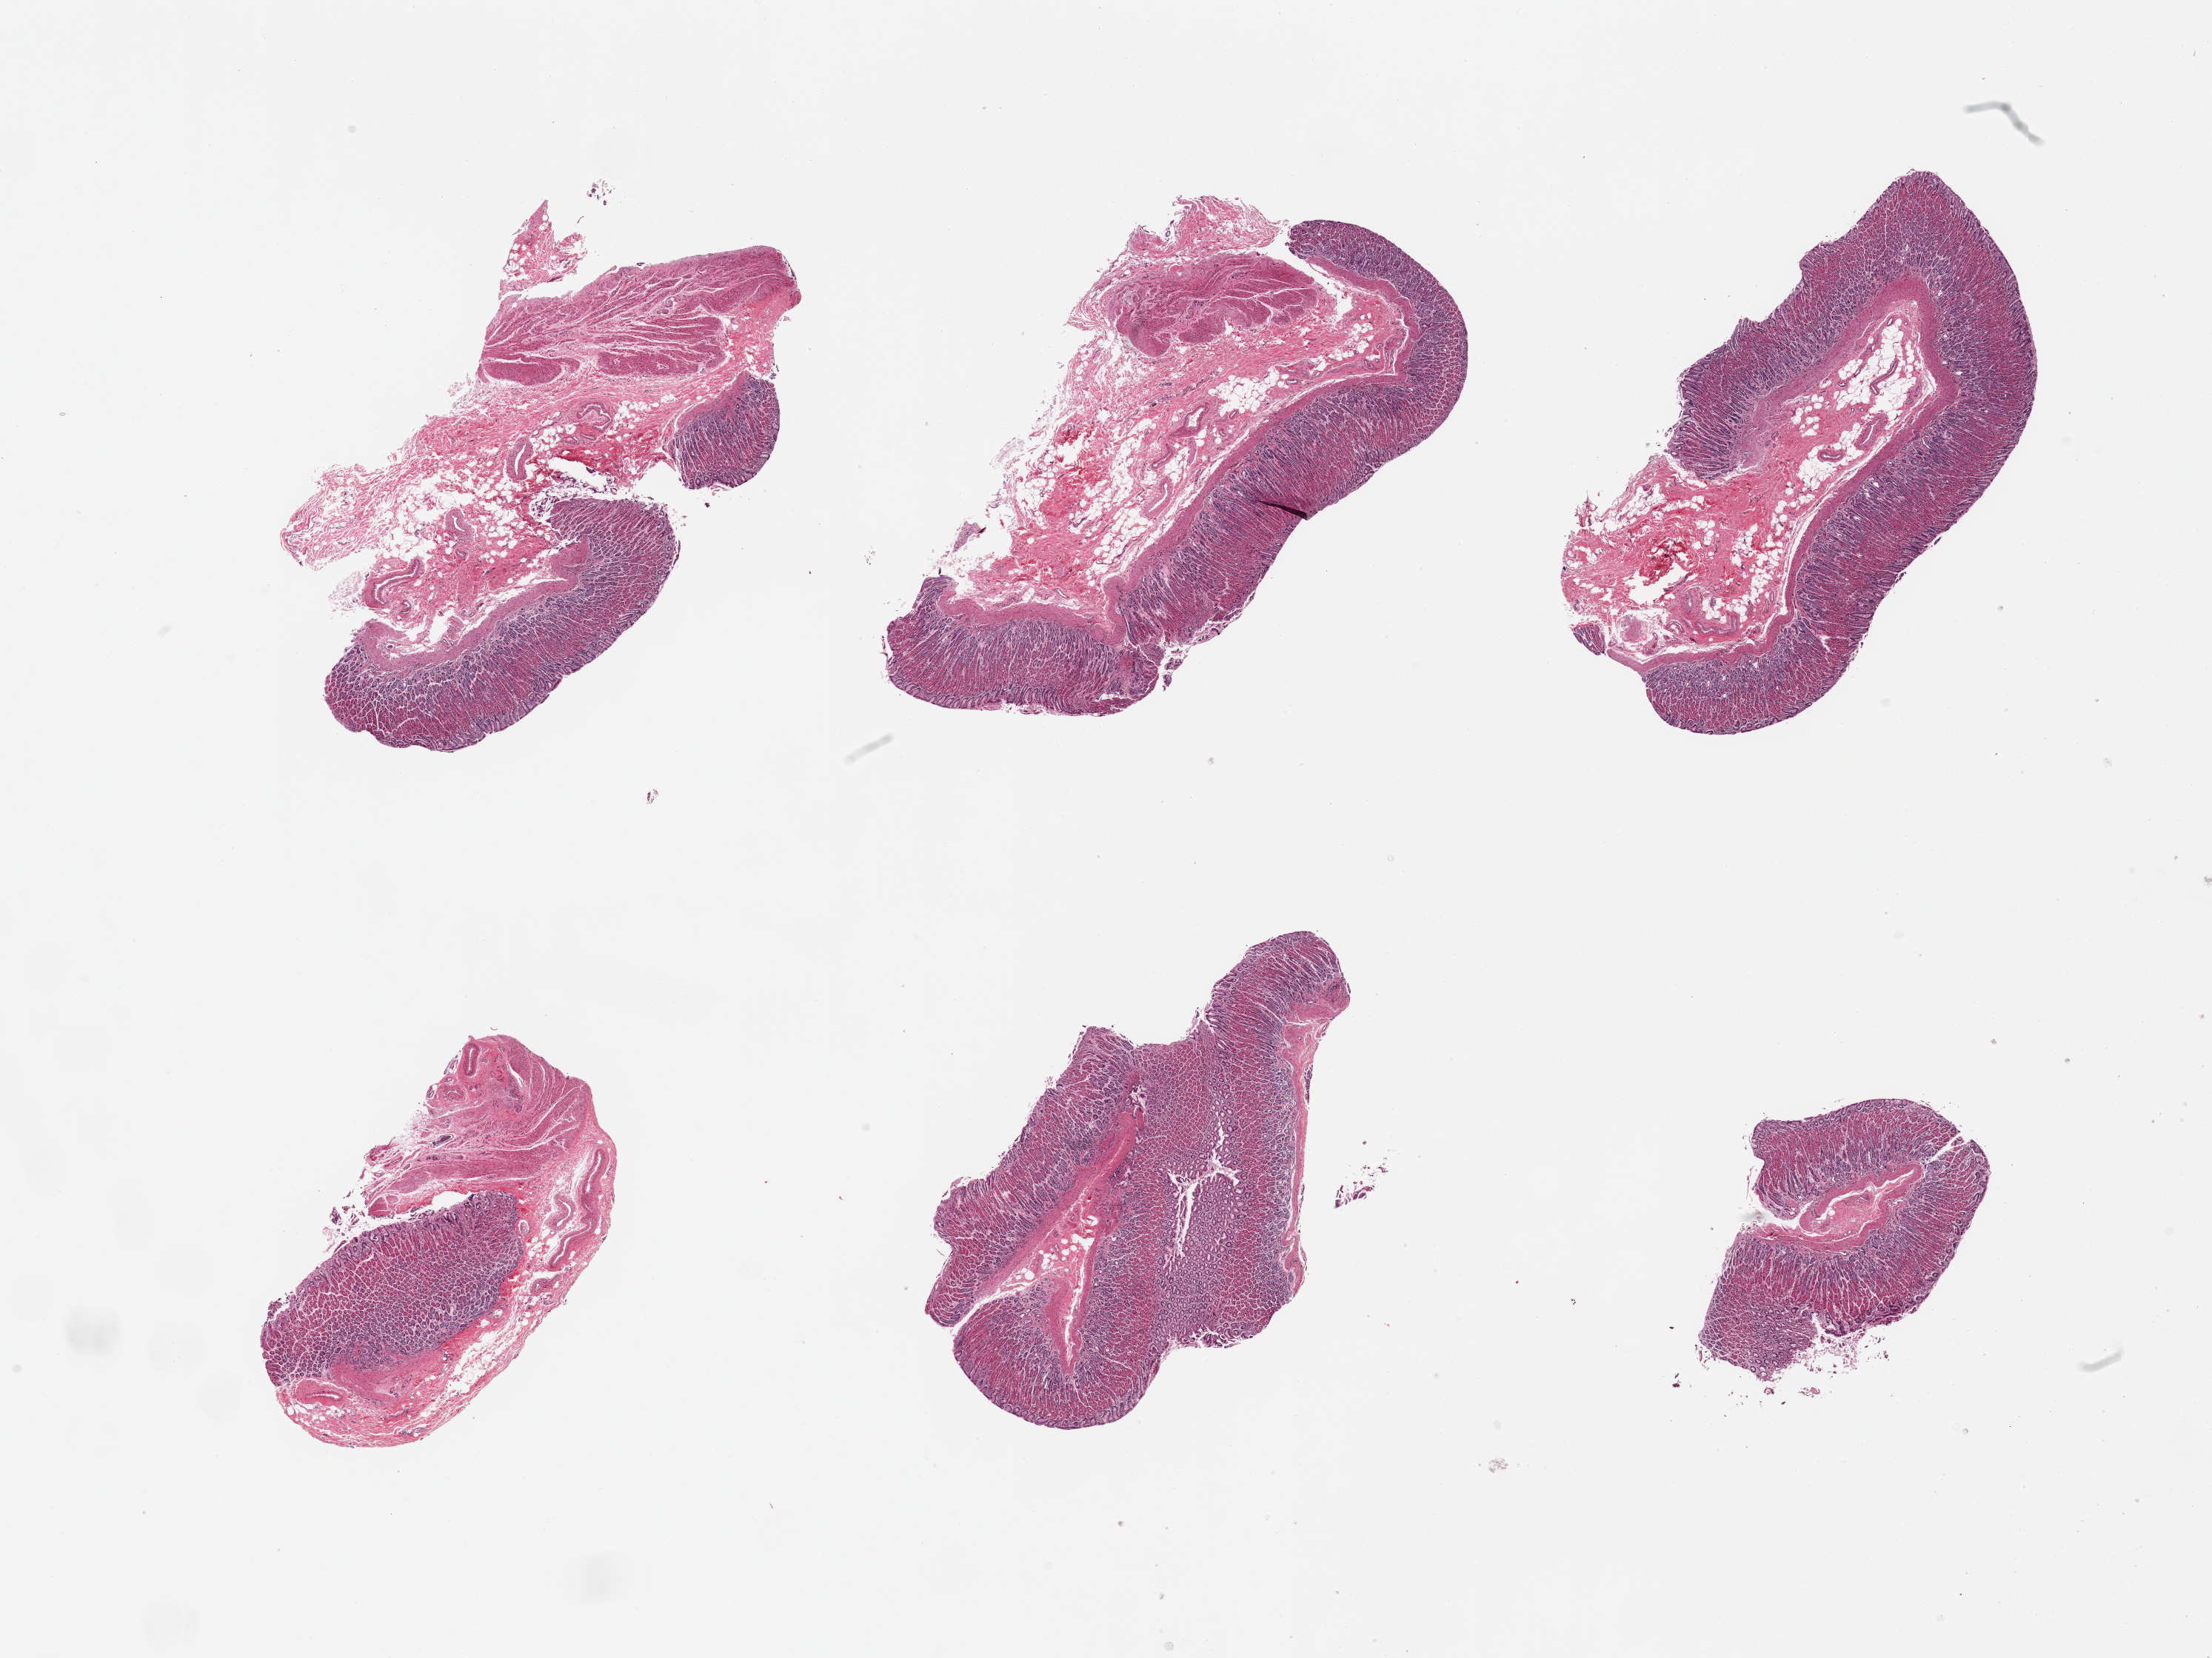
H&E whole-slide image, brightfield — low-resolution overview of the scanned area, about 23.6 x 17.7 mm (slide scanned at 20x). PAXgene-fixed, paraffin-embedded tissue. Sampled site (target tissue): stomach. Tissue donor sample. Female donor.
* reviewer comment on this tissue sample: 6 pieces generally well preserved mucosa, ~1mm layer, ~30-80% thickness